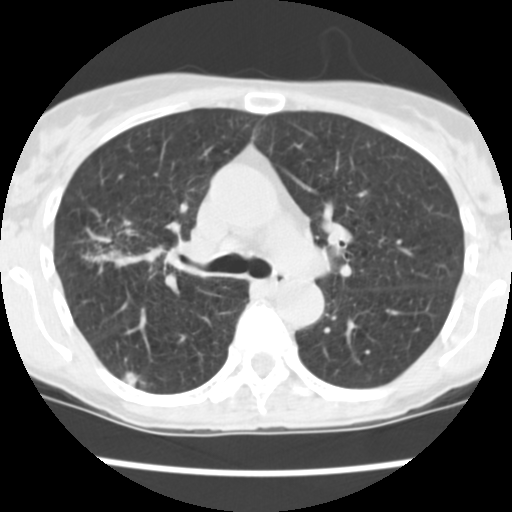
Low-dose screening chest CT, one axial slice. Position 158 of 252 along the scan axis. 120 kVp. Lung window (W 1500 / L -600 HU). 2.5 mm slice thickness. 512 × 512 image matrix.
Outlined on this slice (outlined manually by an expert reader):
- lesion 1 (tumor, upper lobe of right lung): bounding box [x1, y1, x2, y2] px = [122, 372, 138, 386]
- lesion 2 (tumor, lower lobe of right lung): [89, 250, 143, 266]